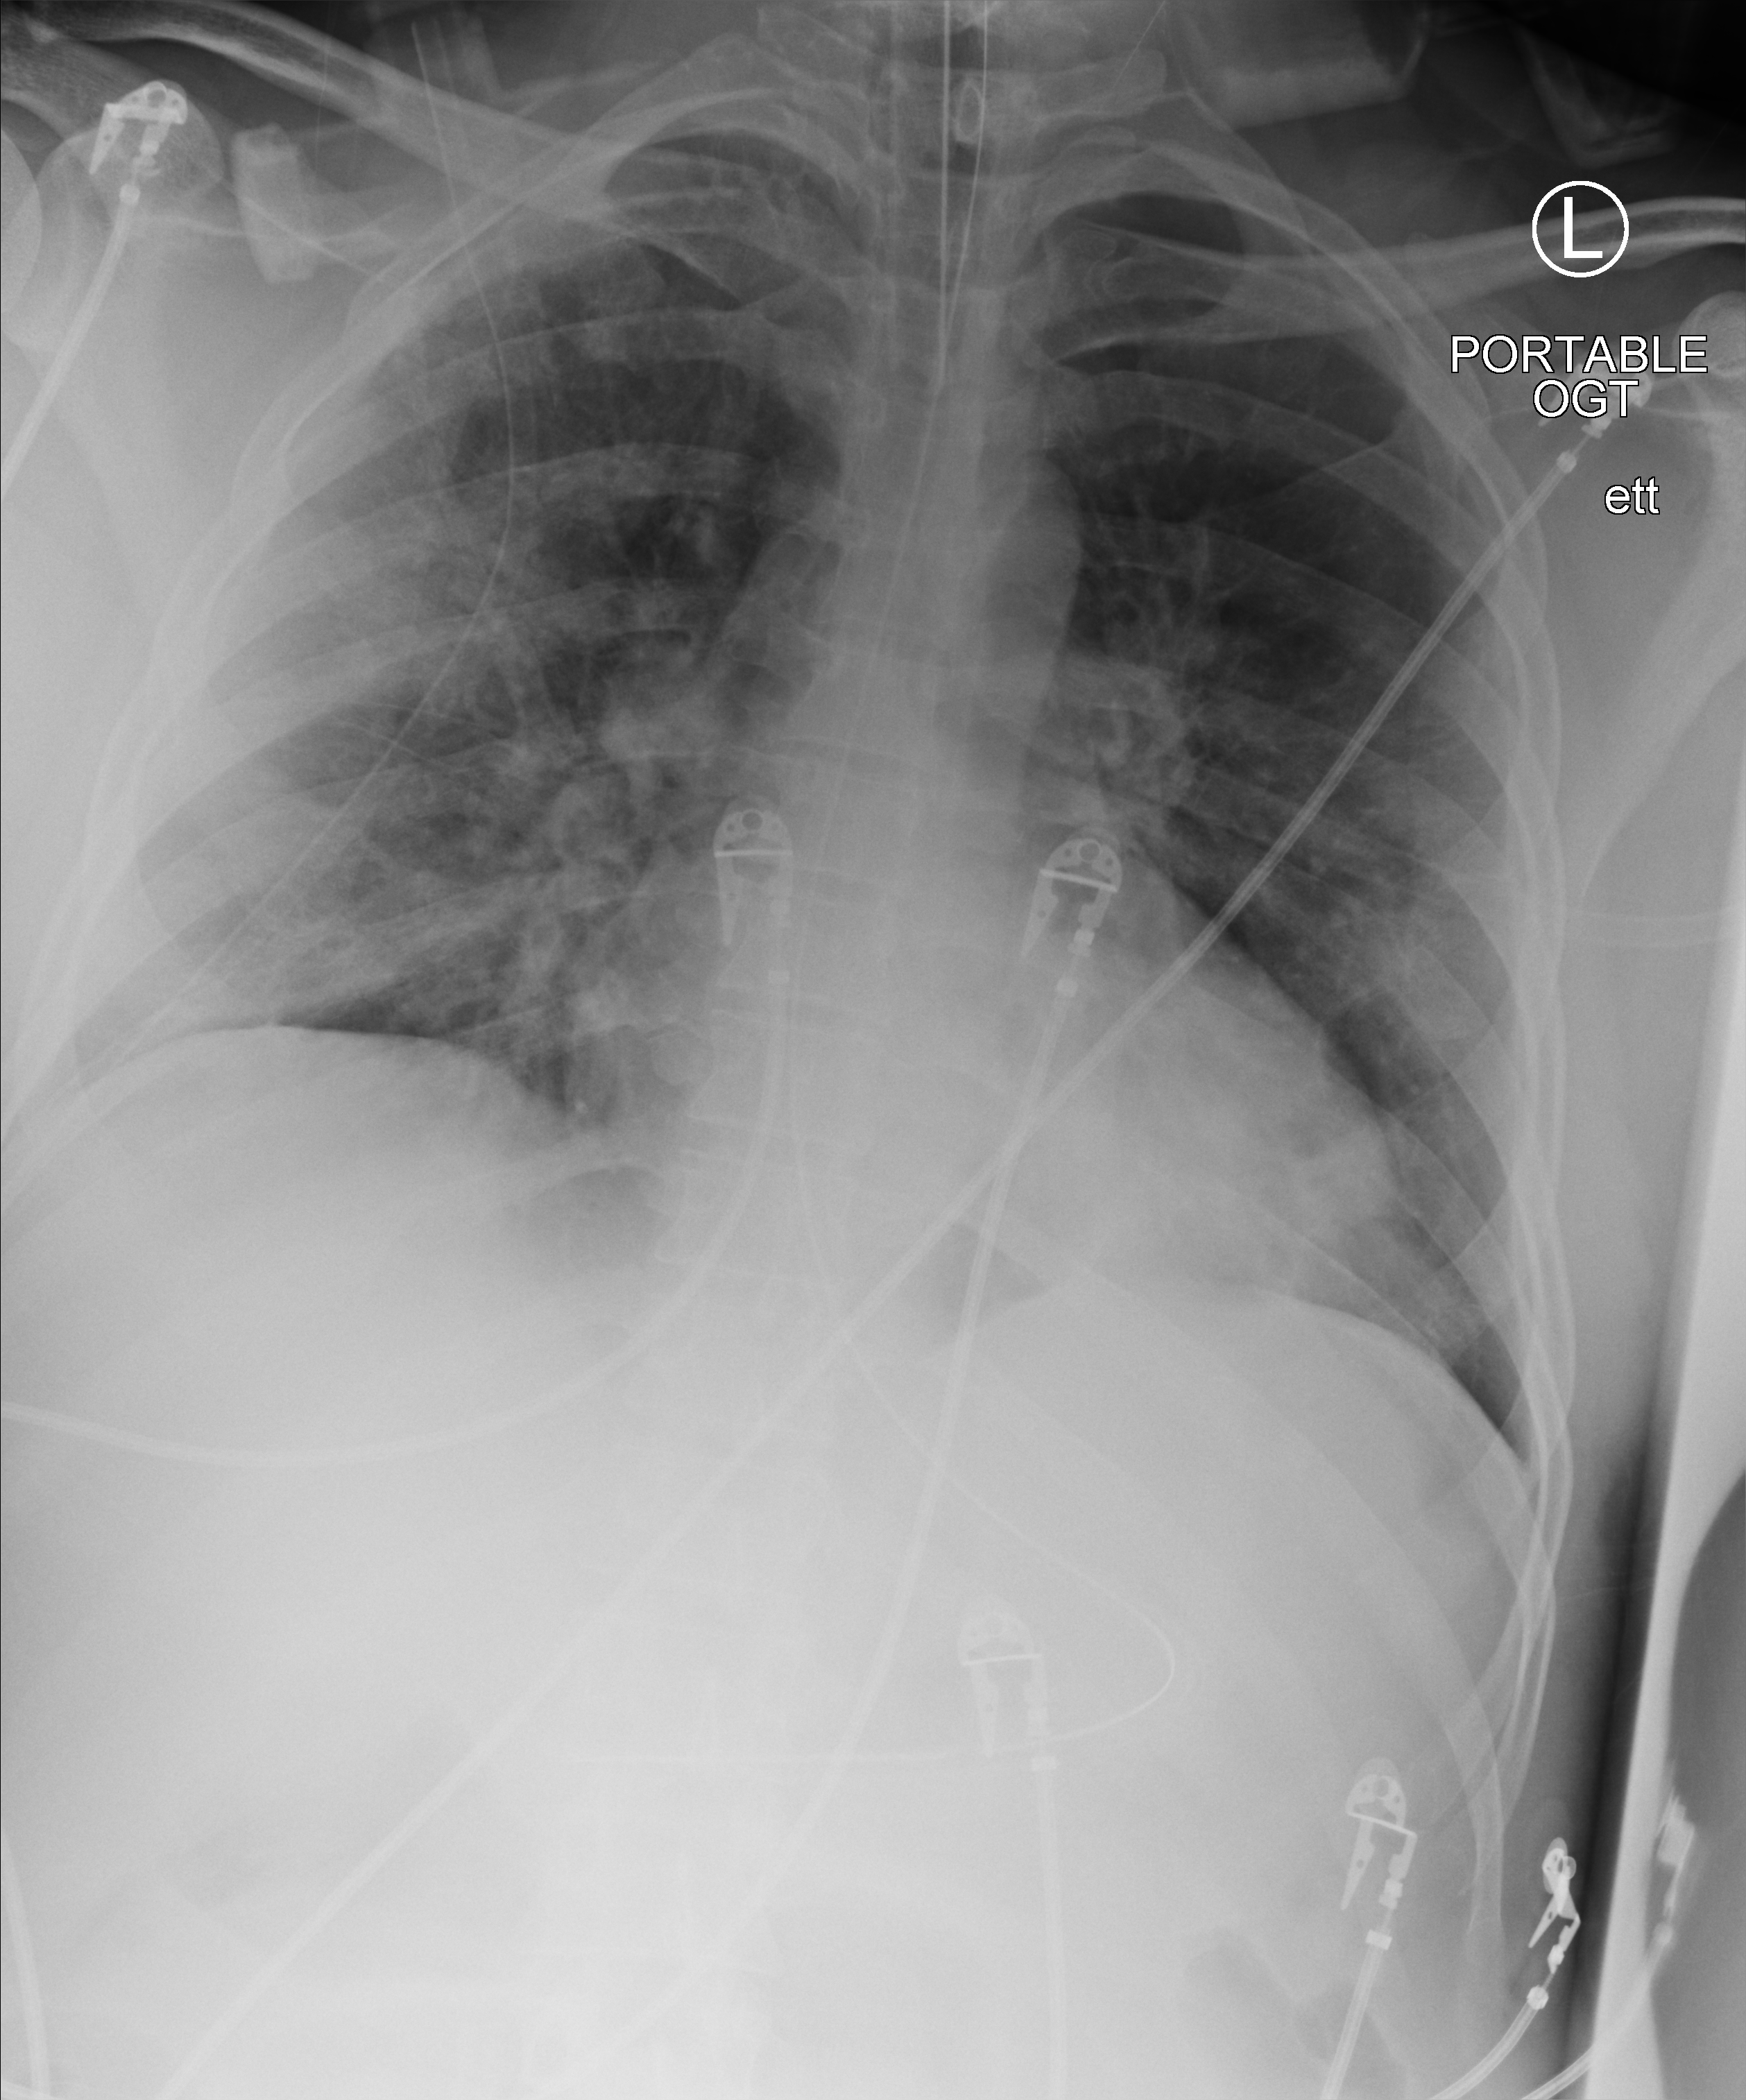
Portable chest radiograph; anteroposterior (AP) projection. Male patient hospitalised with COVID-19, age 18–59 years.
Hospital-stay facts (about this admission, not read from this image; timing relative to this image not recorded): length of hospital stay: 31 days; COPD (admission record): no.